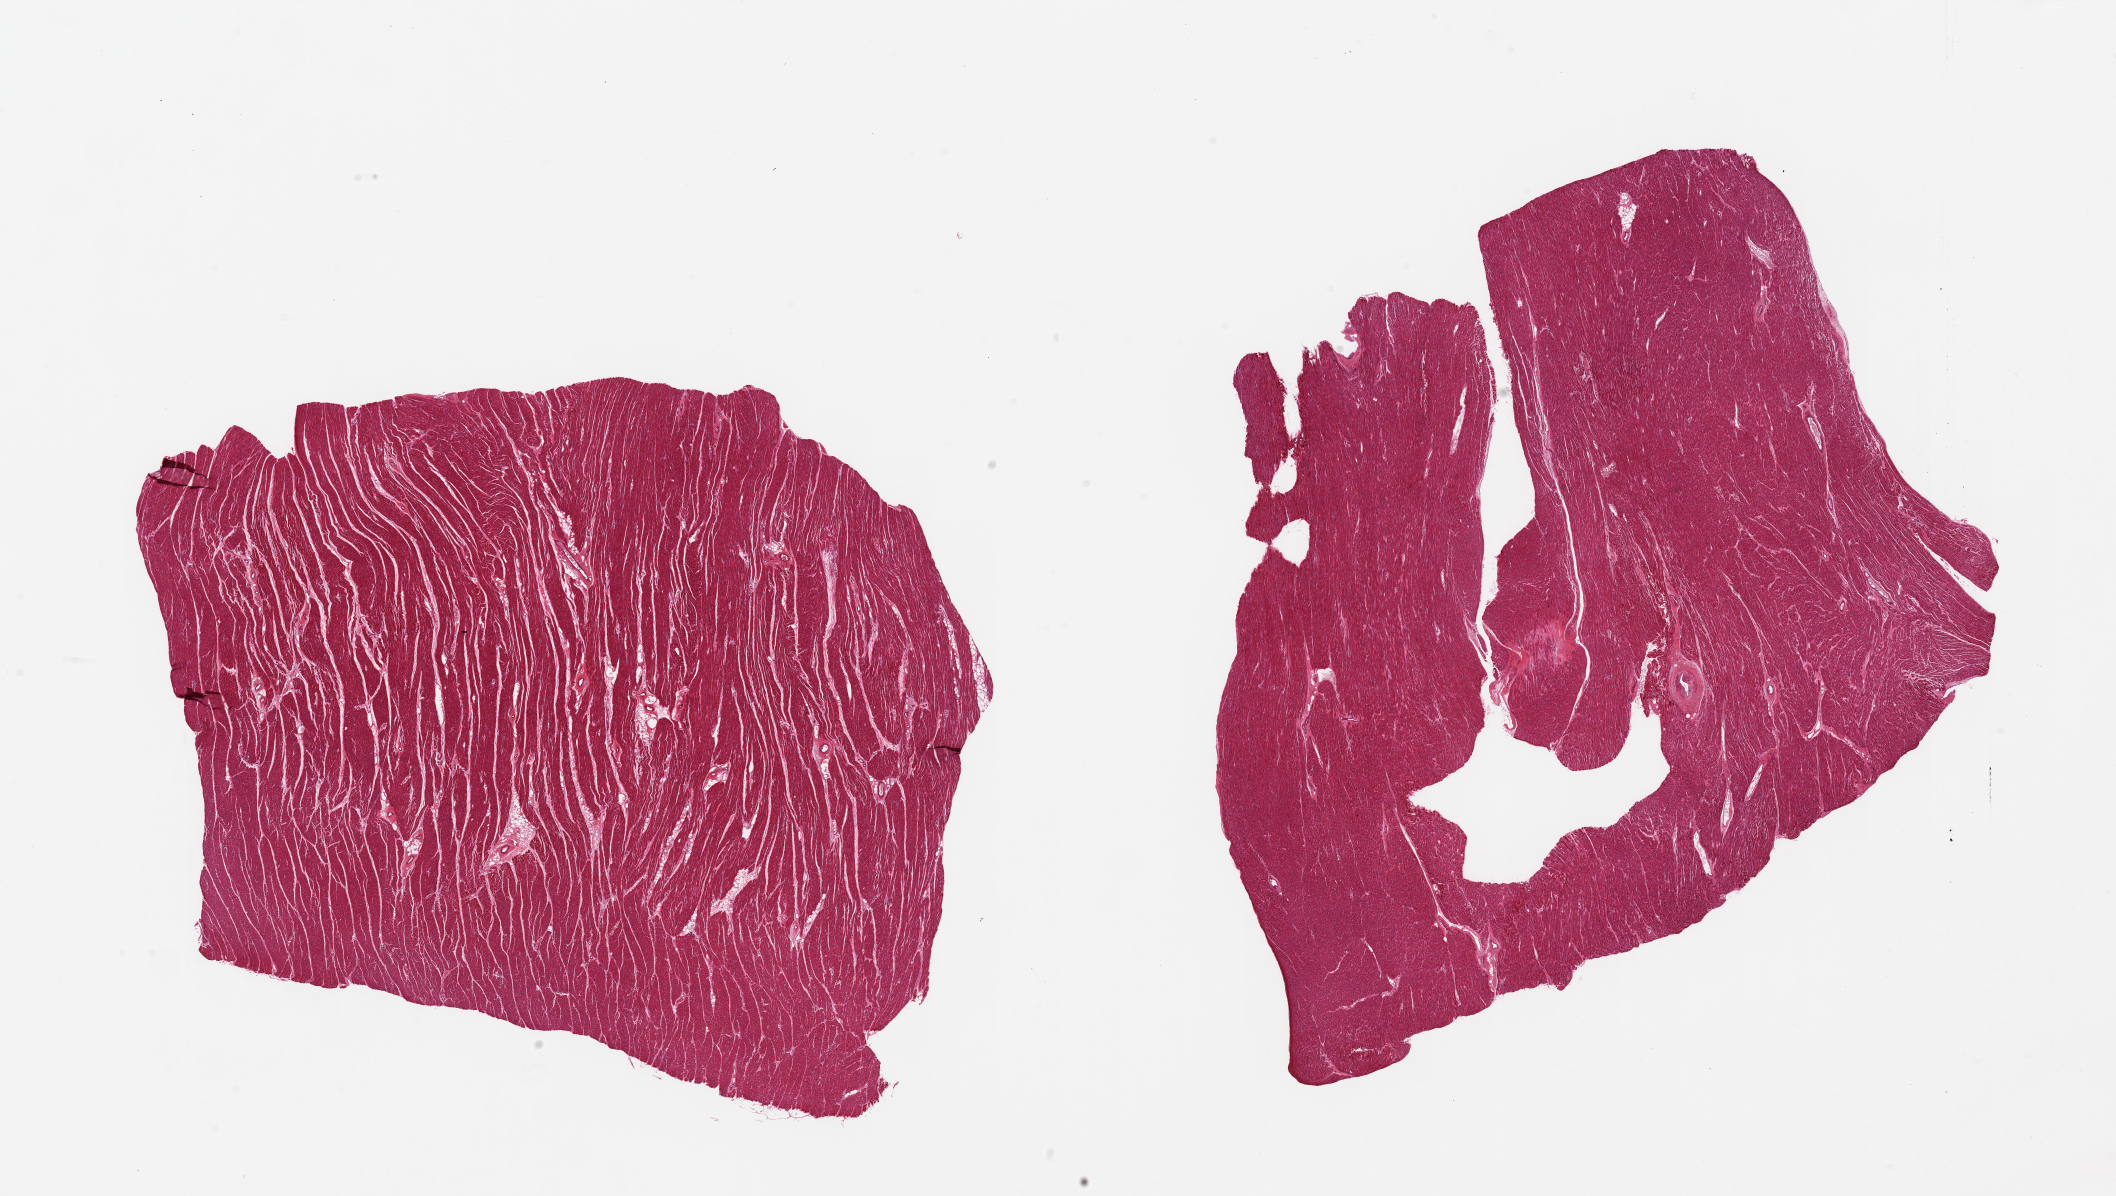
Whole-slide image, haematoxylin and eosin stain — shown as a low-resolution overview of the whole scanned area (about 33.5 x 18.9 mm, acquisition: 20x scan), PAXgene-fixed, paraffin-embedded tissue, sampled site (target tissue): heart, donor tissue sample. Female donor.
* pathologist's review note for this sample: 2 pieces, minimal fibrosis